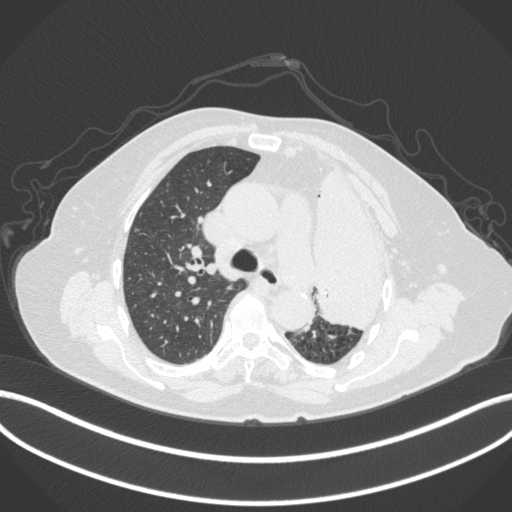
Chest CT, one axial slice. Position 266 of 399 along the scan axis. 120 kVp. Lung window (W 1500 / L -600 HU). 512 × 512 image matrix, field of view 400 × 400 mm. Patient: female, 75 years. Case-level facts recorded for this patient, not image findings: clinical TNM (as recorded): T3 N3 M1.
Annotated regions visible in this slice (bounding box drawn by a radiologist):
- lung tumour (recorded histology: adenocarcinoma): bounding box [x1, y1, x2, y2] px = [308, 161, 394, 338]